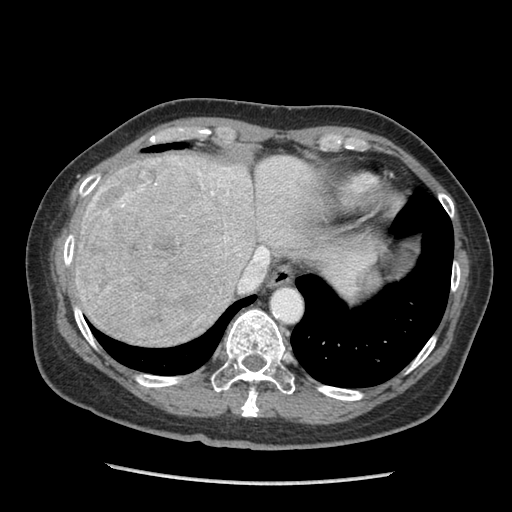
Contrast-enhanced abdominal CT (liver protocol), one axial slice. Slice 76 of 105 in the series (ordered by position). Reconstruction kernel STANDARD. 140 kVp. Soft-tissue window (W 400 / L 40 HU). 512 × 512 image matrix. Case-level facts recorded for this patient, not image findings: diagnosis: hepatocellular carcinoma (patient treated with transarterial chemoembolisation; whether this scan precedes or follows treatment is not stated here); TNM stage (as recorded): Stage-I; Child-Pugh class: A; tumour differentiation: moderately differentiated.
Outlined on this slice (semi-automatic segmentation, software-assisted and operator-edited):
- liver parenchyma outside the tumour (the mass and vessels are separate outlines, so this box may not span the whole liver): bounding box (x1, y1, x2, y2) in pixels: (74, 152, 338, 330)
- mass: (75, 155, 231, 345)
- liver vessels: (95, 169, 230, 199)